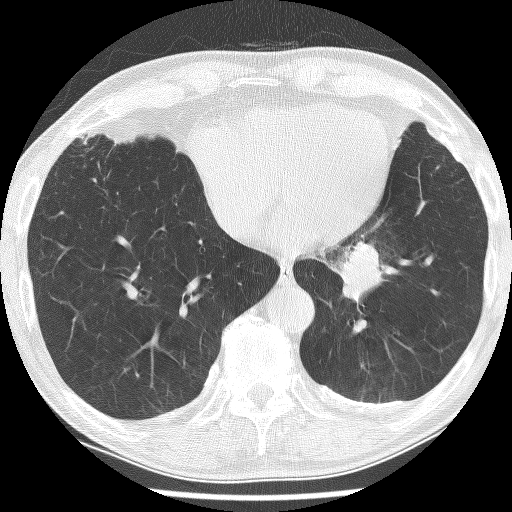
Low-dose screening chest CT, one axial slice; position 55 of 226 along the scan axis; reconstruction kernel BONE; 120 kVp; lung window (W 1500 / L -600 HU); 2.5 mm slice thickness; 512 × 512 image matrix, field of view 320 × 320 mm.
Structures marked on this image (outlined manually by an expert reader):
- lesion 1 (tumor, lower lobe of left lung): bounding box (x1, y1, x2, y2) in pixels: (341, 241, 383, 301)